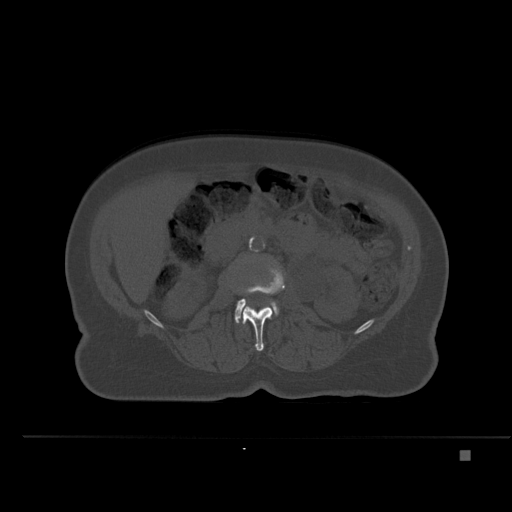
CT including the spine, one axial slice. Slice 210 of 477 in the series (ordered by position). Bone window (W 1800 / L 400 HU). 1.5 mm slice thickness. 512 × 512 image matrix, field of view 422 × 422 mm. Female patient, age 74 years. From the clinical record (not read from this slice): primary cancer: colon.
Structures marked on this image (semi-automatically segmented with operator editing):
- L2 vertebra: bounding box [x1, y1, x2, y2] px = [242, 265, 285, 351]
- L3 vertebra: [235, 299, 279, 323]